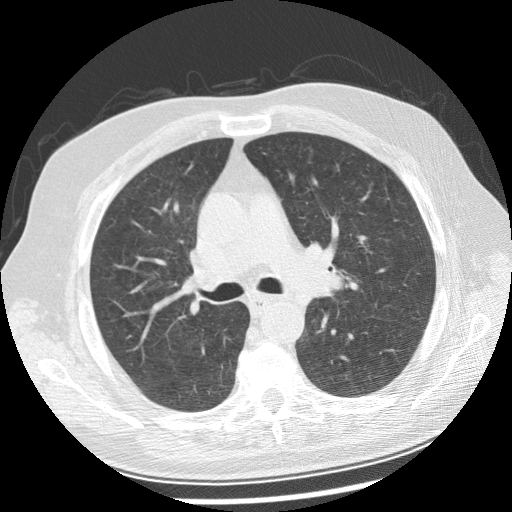
Low-dose screening chest CT, one axial slice. Slice 156 of 250 in the series (ordered by position). Reconstruction kernel STANDARD. Lung window (W 1500 / L -600 HU). 512 × 512 image matrix.
Annotated regions visible in this slice (expert manual segmentation):
- lesion 1 (tumor, left main bronchus): bounding box (x1, y1, x2, y2) in pixels: (310, 271, 345, 297)